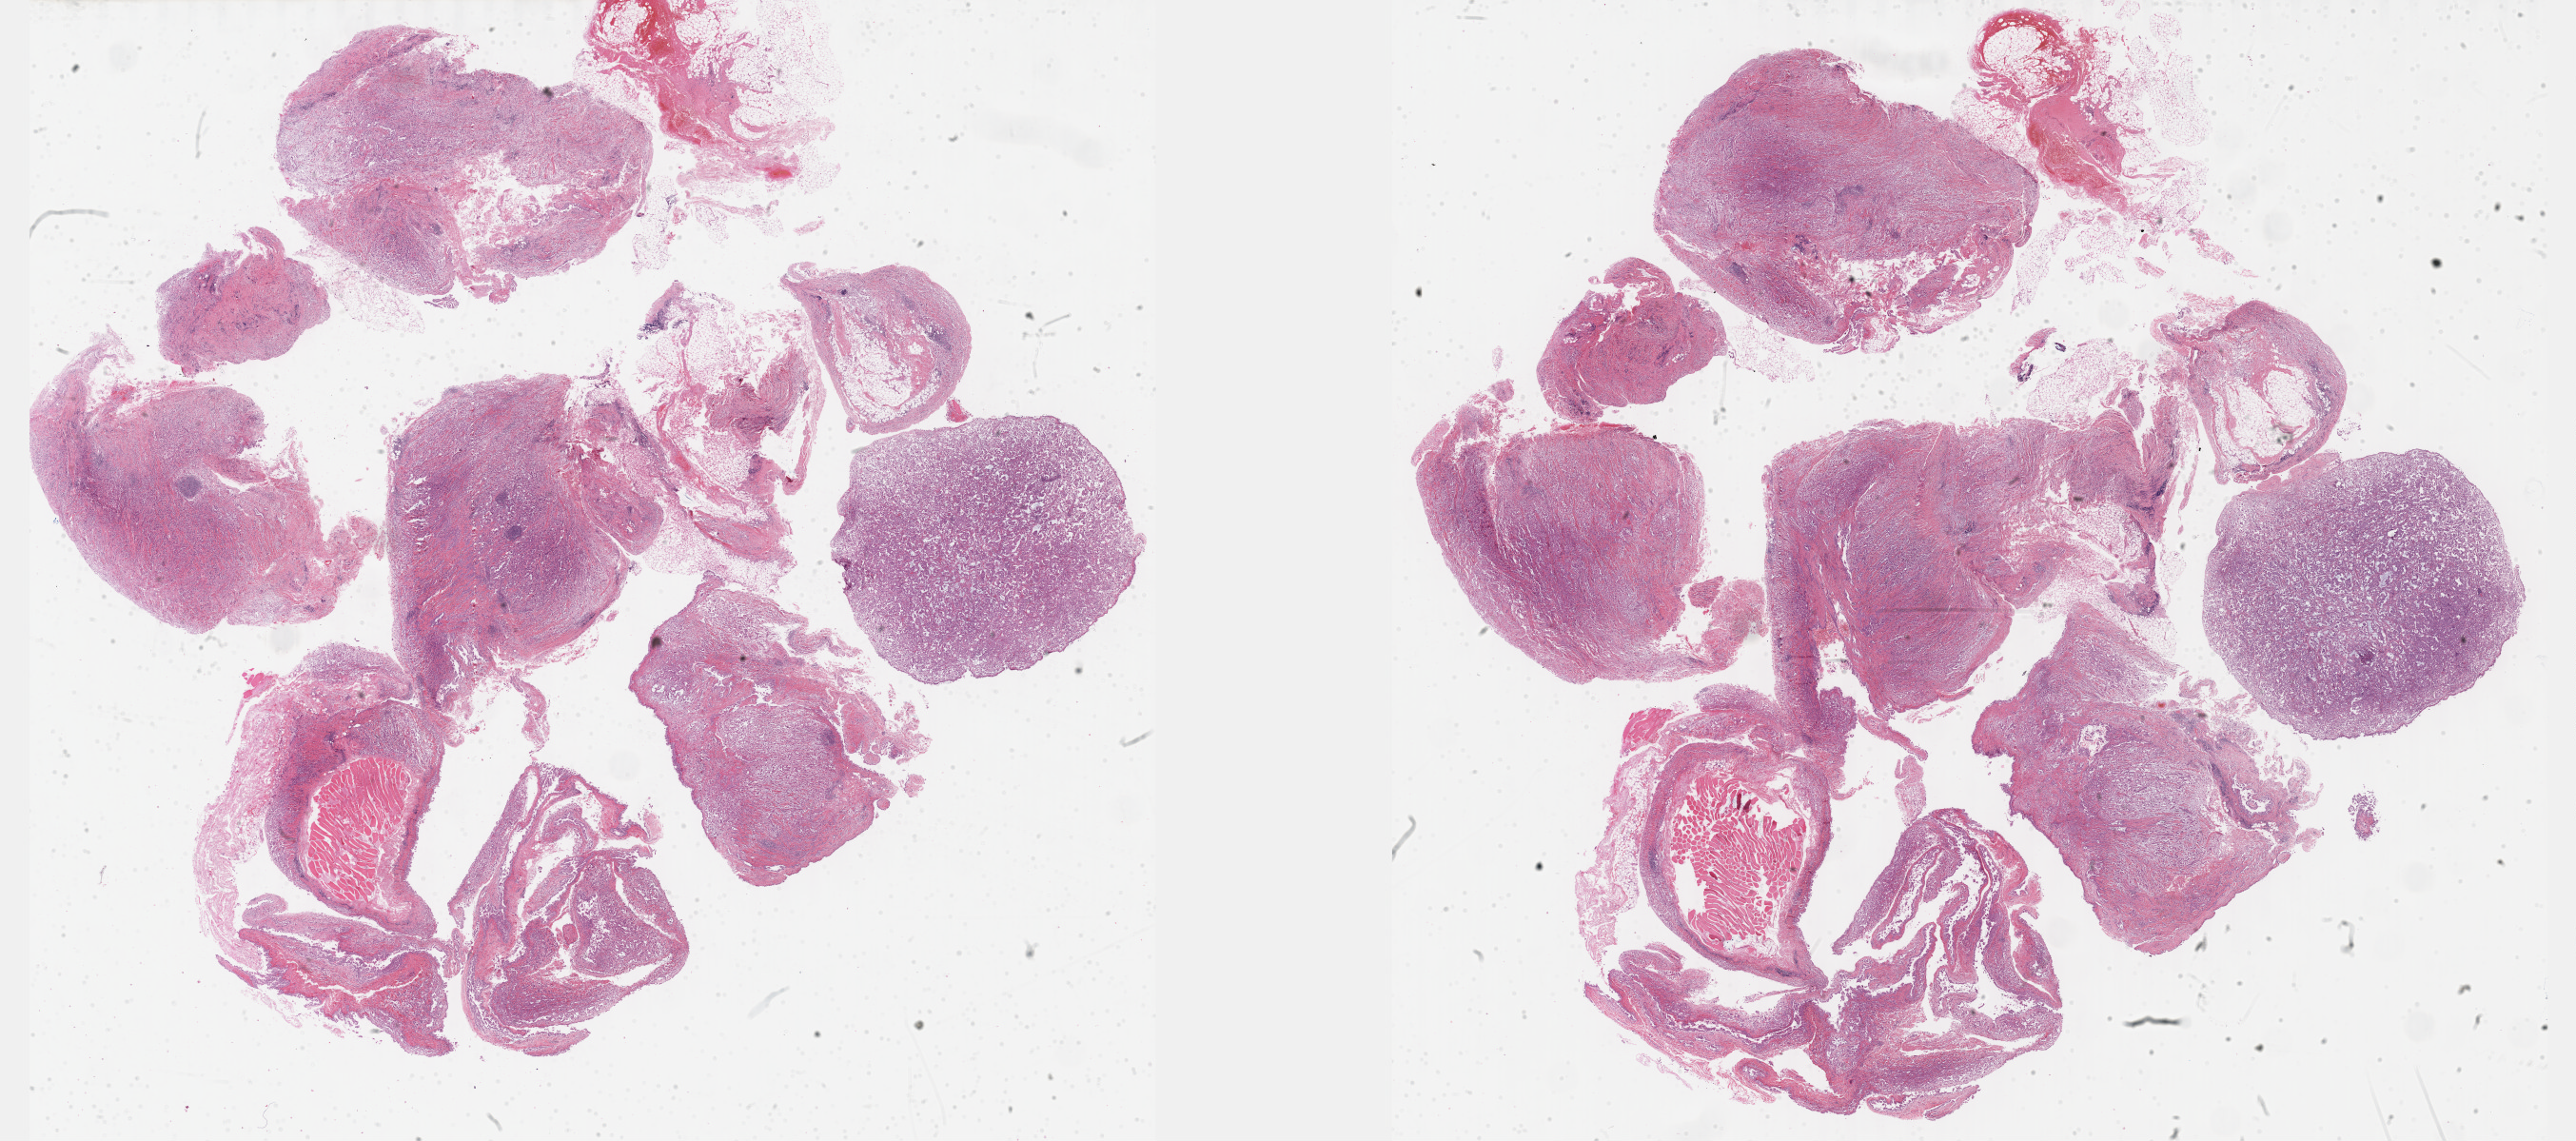
Digitized H&E tissue section (whole slide), shown as a low-resolution overview of the whole scanned area (about 43.8 x 19.4 mm, slide scanned at 40x). Formalin-fixed paraffin-embedded (FFPE) diagnostic section. Sample: primary tumour, mesothelium. Male, age 62 years at initial diagnosis.
Diagnosis: Epithelioid mesothelioma, malignant (pleura, NOS).